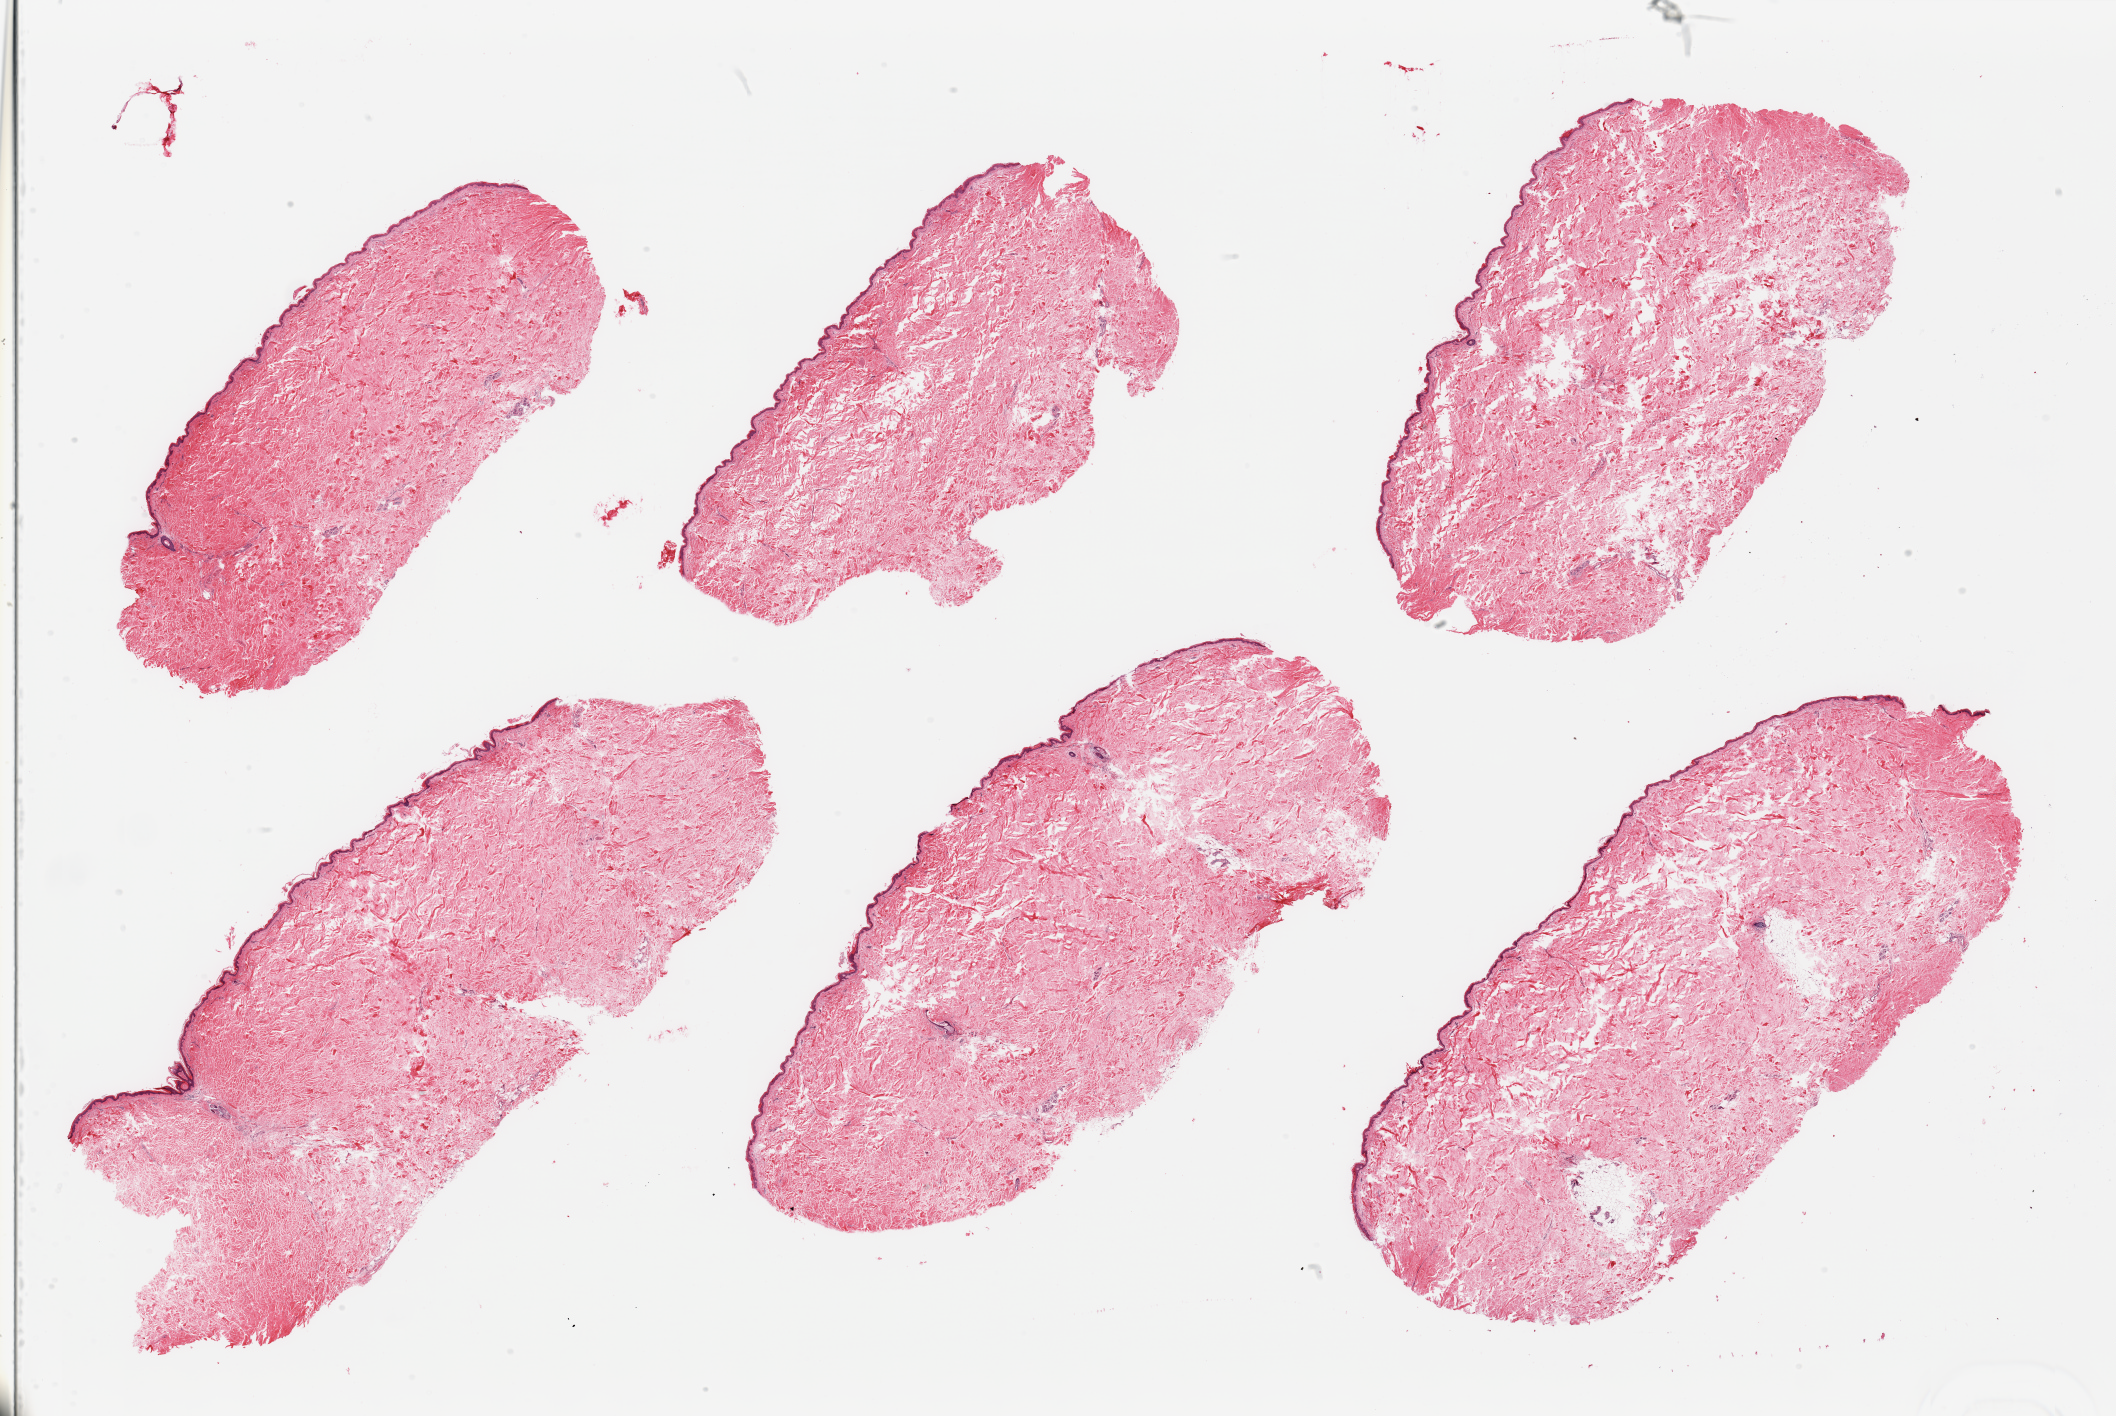
Whole-slide image, haematoxylin and eosin stain, brightfield — a low-resolution overview of the entire scanned area, about 33.5 x 22.4 mm, PAXgene-fixed paraffin-embedded (PFPE) section, section of skin of suprapubic region (target tissue), tissue donor sample. Donor: male.
• reviewer comment on this tissue sample: 6 pieces; small focus of seborrheic keratosis; well trimmed; minimal dermal fat